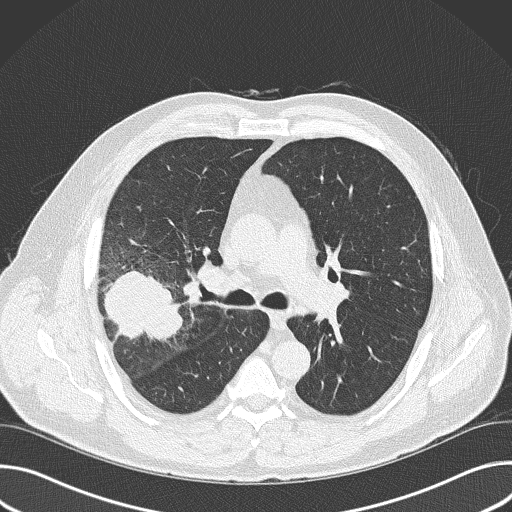
Chest CT (low-dose screening protocol), one axial image. Baseline annual screen. Lung window (W 1500 / L -600 HU). Lung (sharp) reconstruction kernel (B50f). 120 kVp. Slice 101 of 157 in the series. 512 × 512 image matrix. Male participant, aged 56 years at enrolment. Current smoker at enrolment.
Expert reader's lesion annotation, box from (x=81, y=261) to (x=185, y=367) px. Reader record for this screening exam (exam-level; its link to the box is not recorded): non-calcified nodule or mass ≥4 mm, right upper lobe, 6 × 5 mm, spiculated (stellate) margins, soft tissue attenuation. Lung cancer was diagnosed 16 days after this screen: adenocarcinoma, NOS, right upper lobe, poorly differentiated (G3), stage IIB (AJCC 6th edition), 60 mm at pathology.